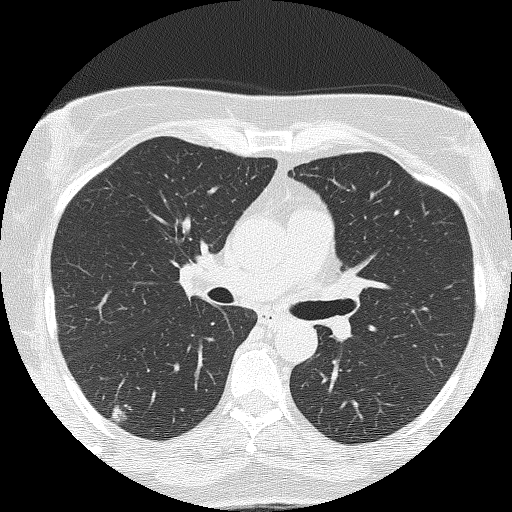
Low-dose screening chest CT, axial slice. Second screening round (one year after baseline). Lung window (W 1500 / L -600 HU). Lung (sharp) reconstruction kernel (FC51). 120 kVp. Slice 61 of 143 in the series. Female participant, aged 58 years at enrolment. Former smoker at enrolment.
Lesion marked by an expert reader, bounding box [x1, y1, x2, y2] px = [86, 396, 144, 436]. The screening reader recorded 2 non-calcified nodules or masses ≥4 mm on this exam (right upper lobe, right upper lobe); which of them this box marks is not recorded. Official screen result: positive, other. Later outcome: lung cancer diagnosed 264 days after this screen — adenocarcinoma, NOS, right lower lobe, well differentiated (G1), stage IB (AJCC 6th edition), 10 mm at pathology.